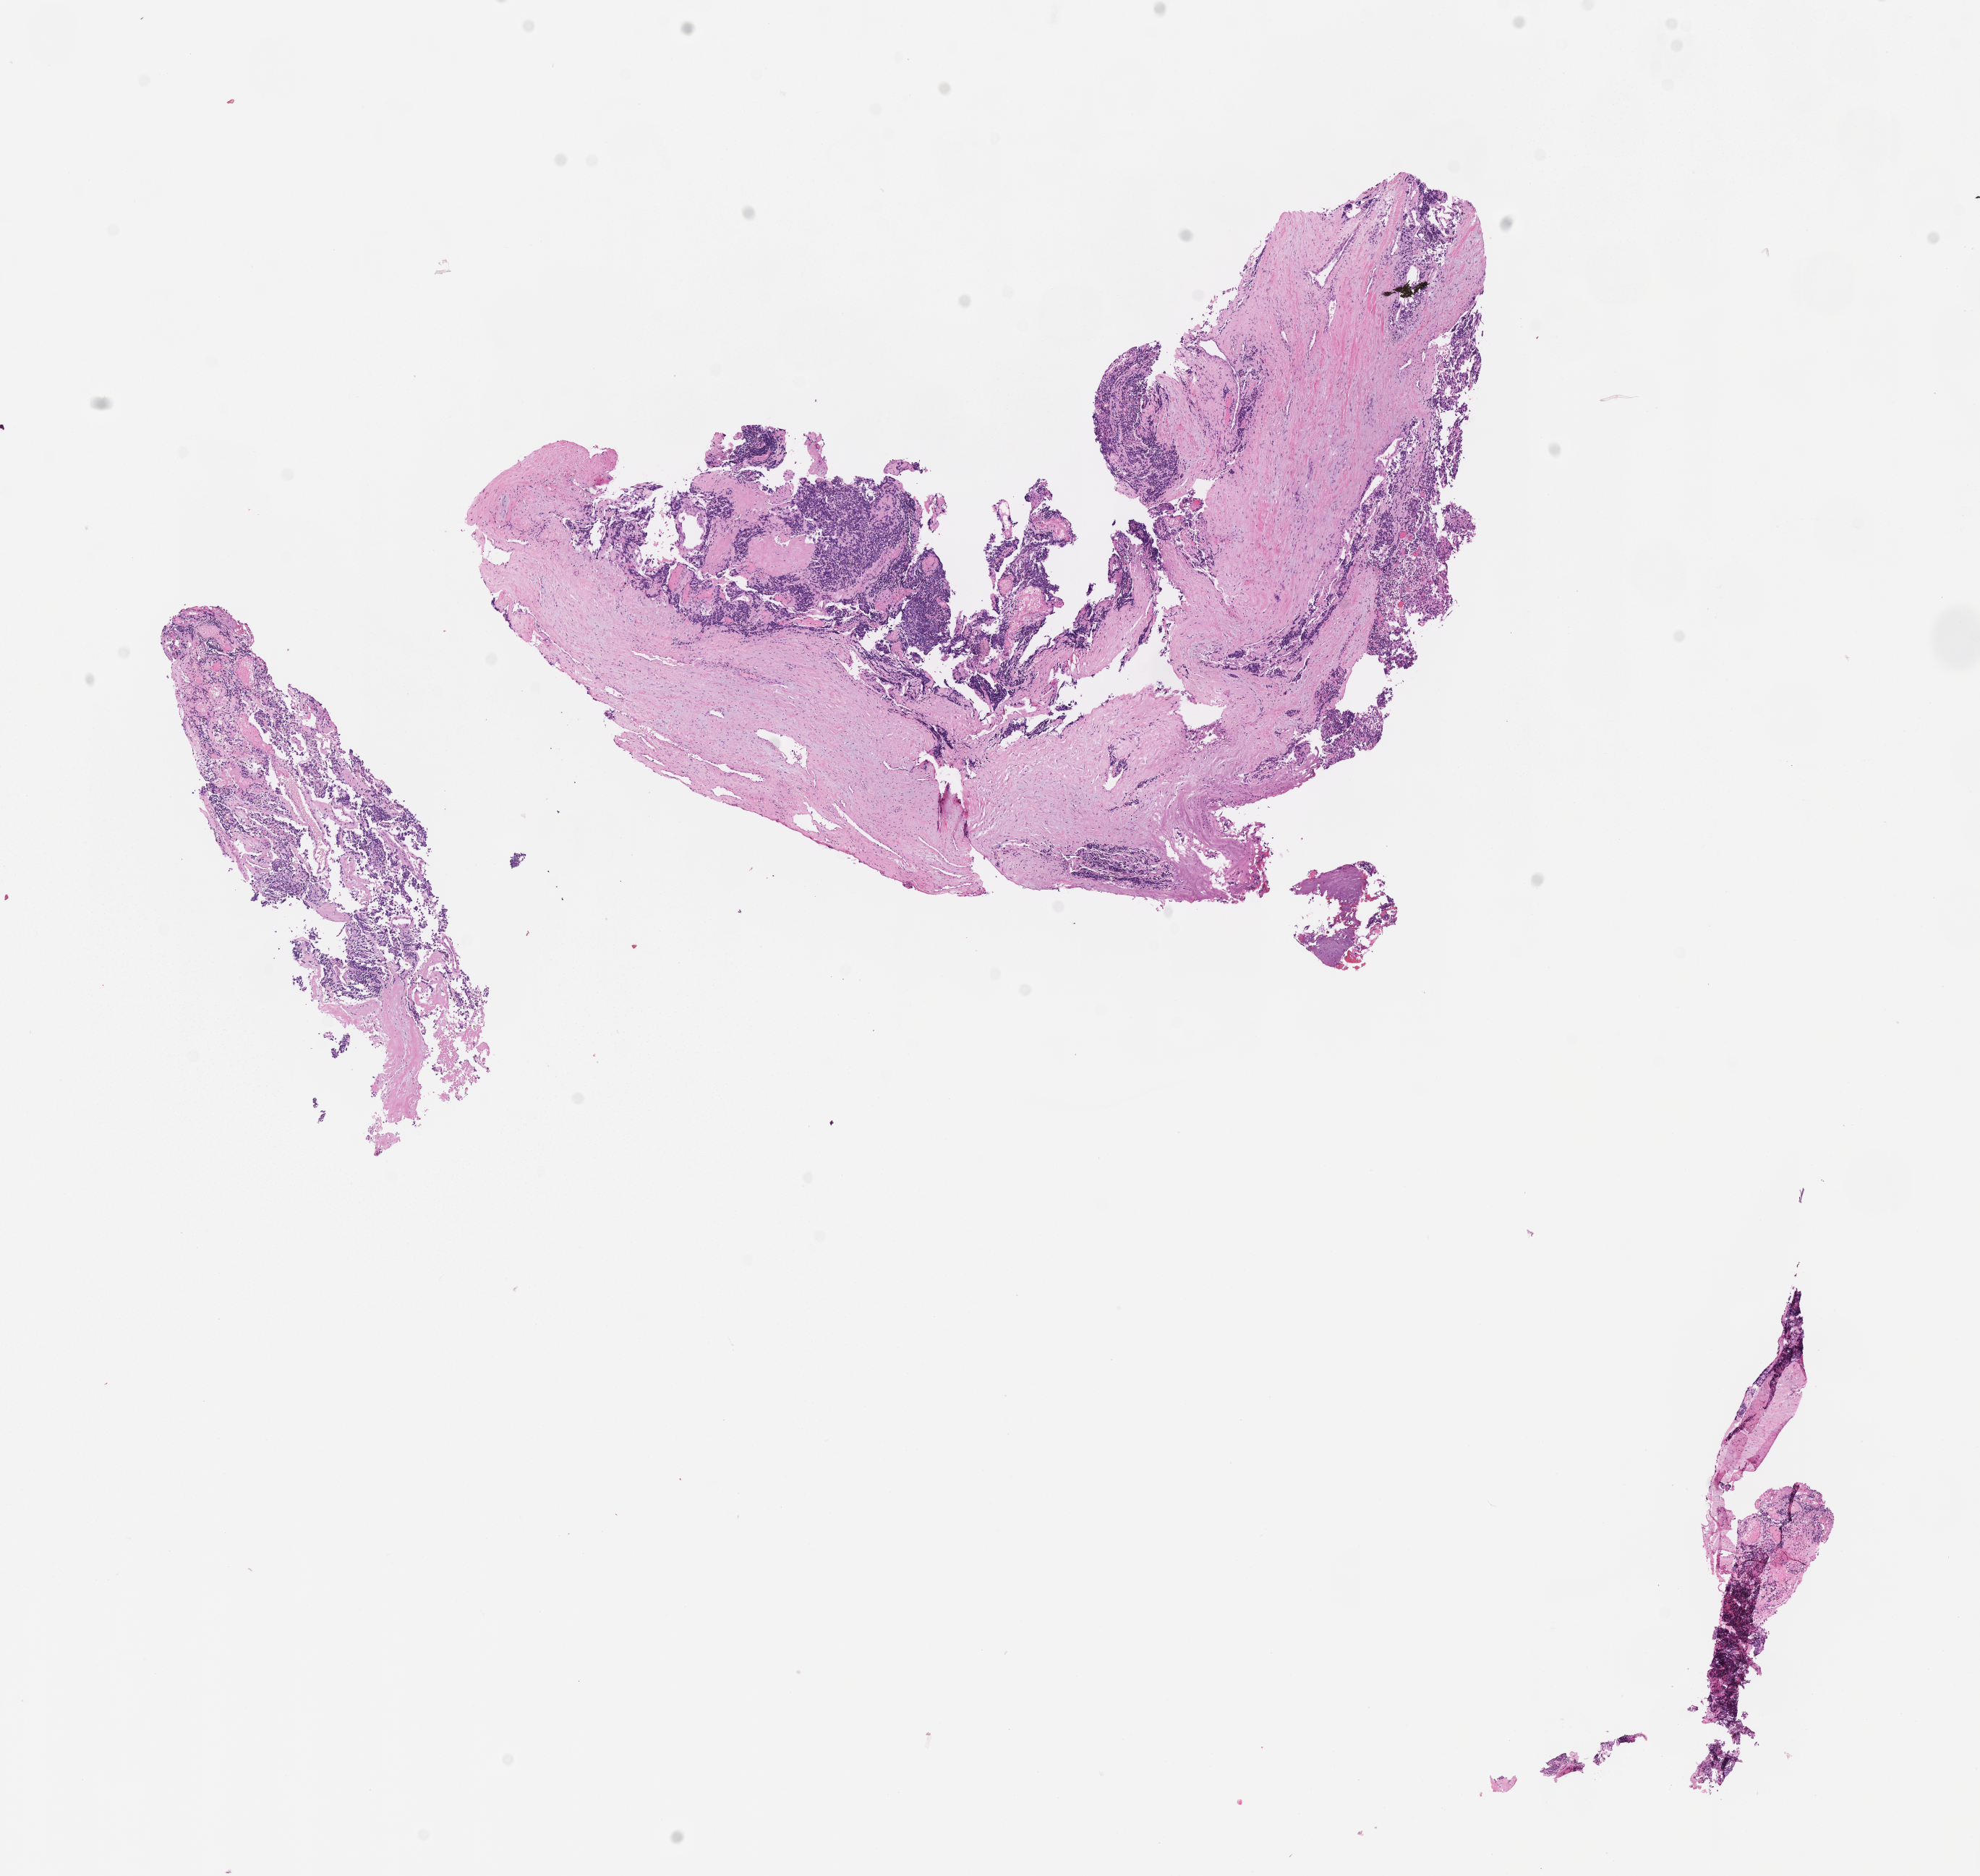
Whole-slide image, haematoxylin and eosin stain of tumor tissue — shown as a low-resolution overview of the whole scanned area (about 11.1 x 10.5 mm). FFPE section. Site: neck. Female patient, age at diagnosis 4.7 years.
Diagnosis: rhabdomyosarcoma; histological classification: alveolar rhabdomyosarcoma.